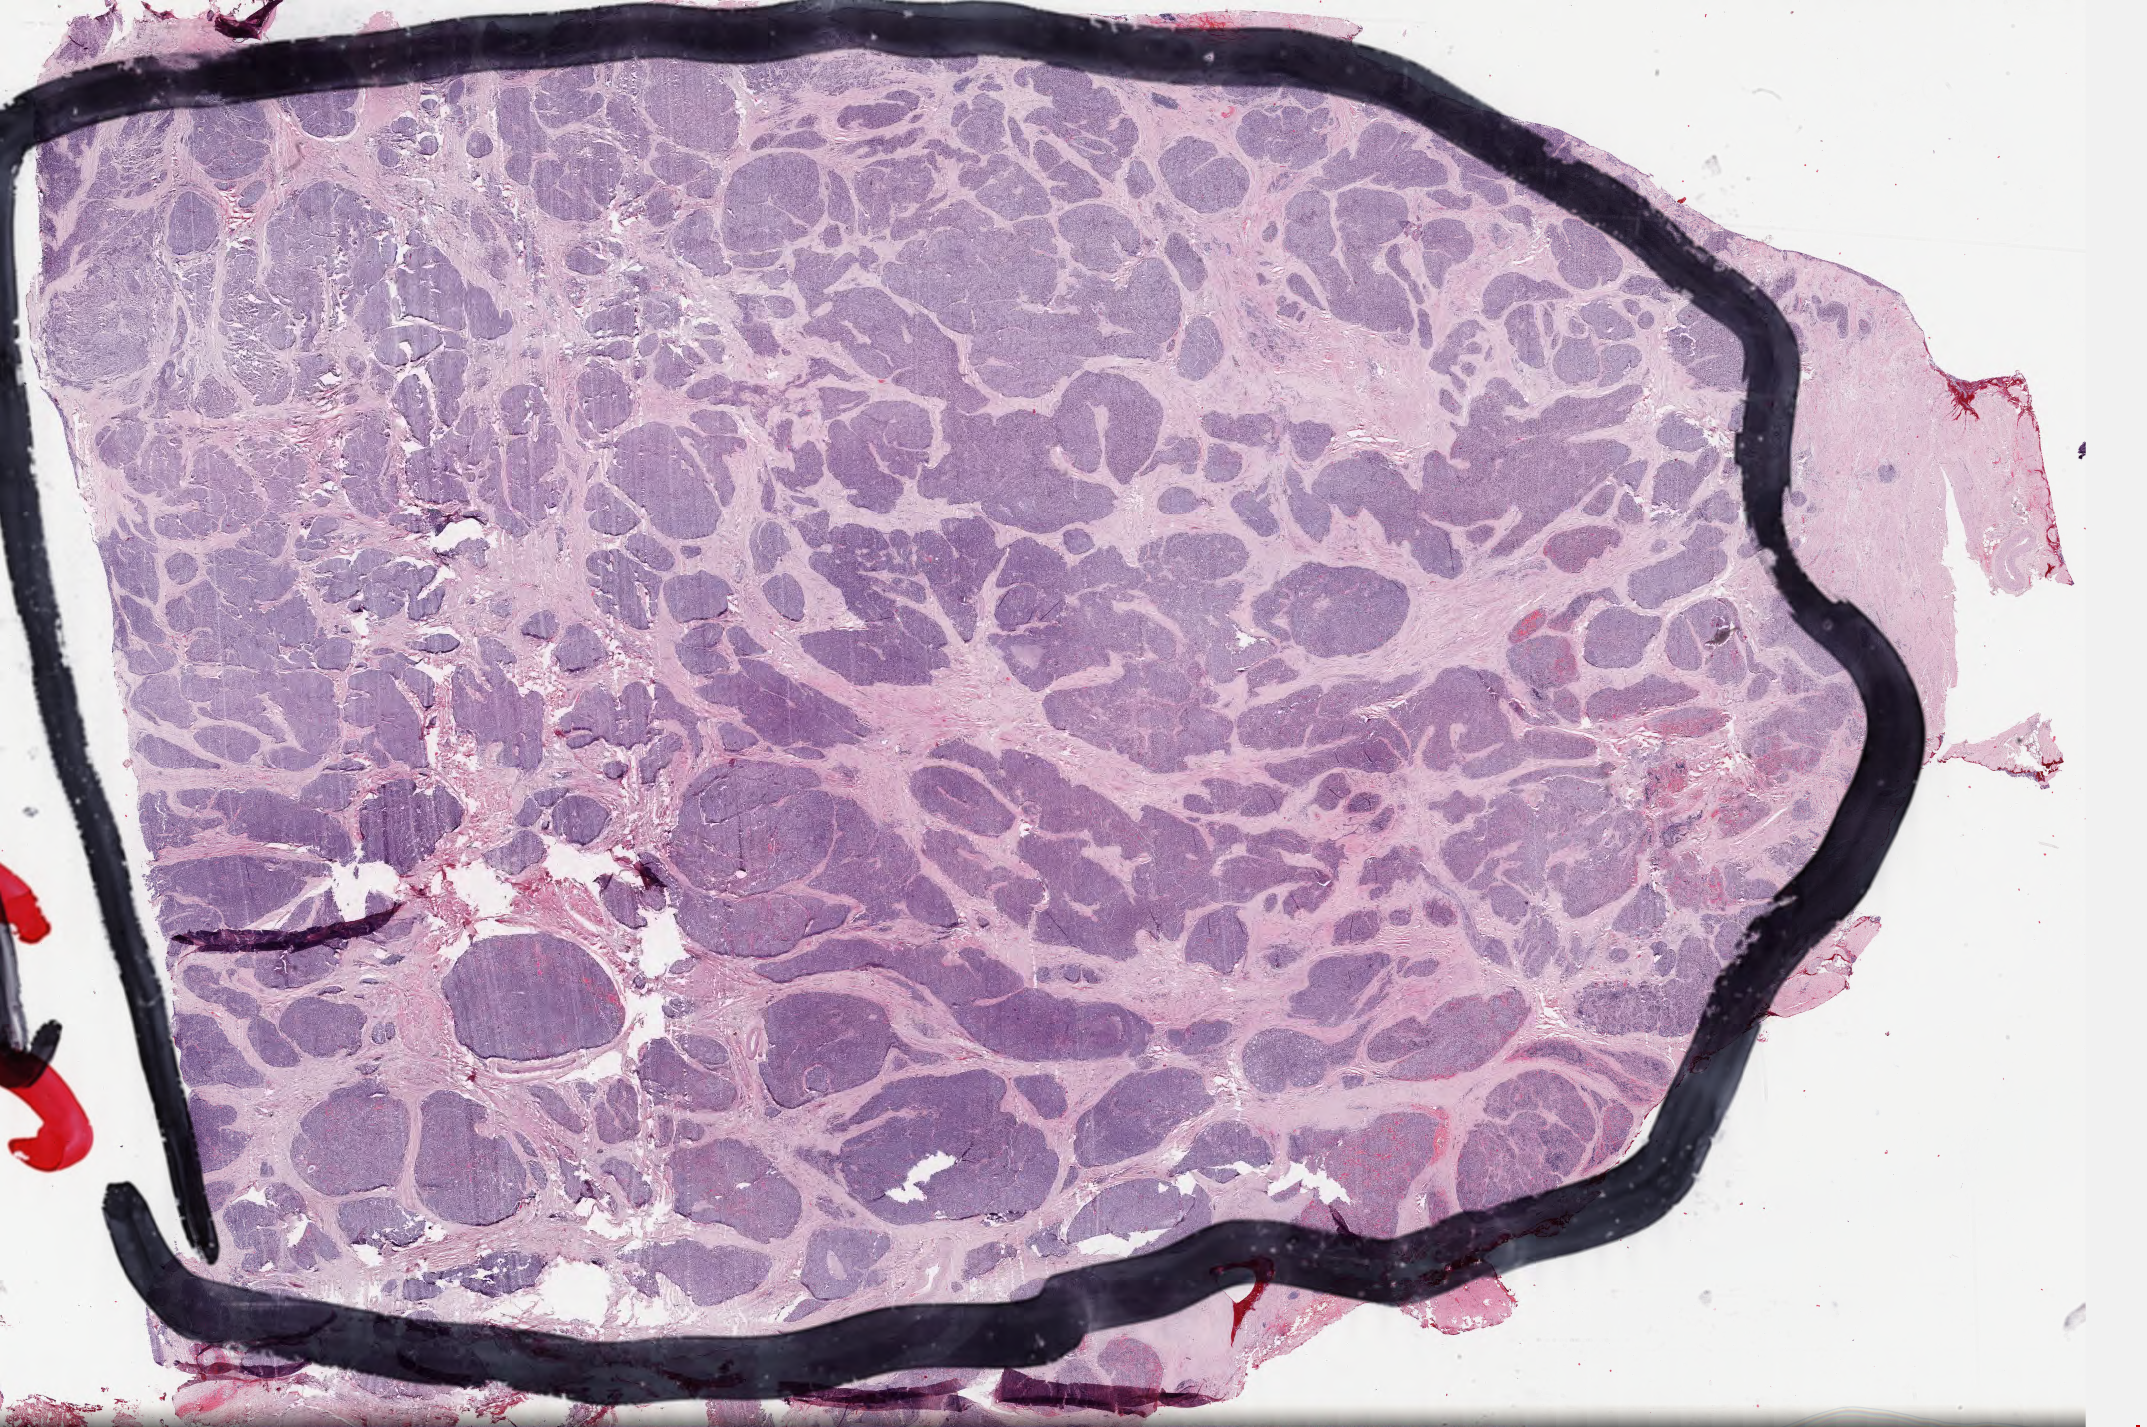
Digitized H&E tissue section (whole slide), whole scanned area (about 34.2 x 22.7 mm) shown as a low-resolution overview. Formalin-fixed paraffin-embedded (FFPE) diagnostic section. Sample: primary tumour, prostate. Male patient; age at initial diagnosis 58 years. Gleason score: 9 (4+5).
Histologic diagnosis: Adenocarcinoma, NOS (prostate gland). Laterality: bilateral.